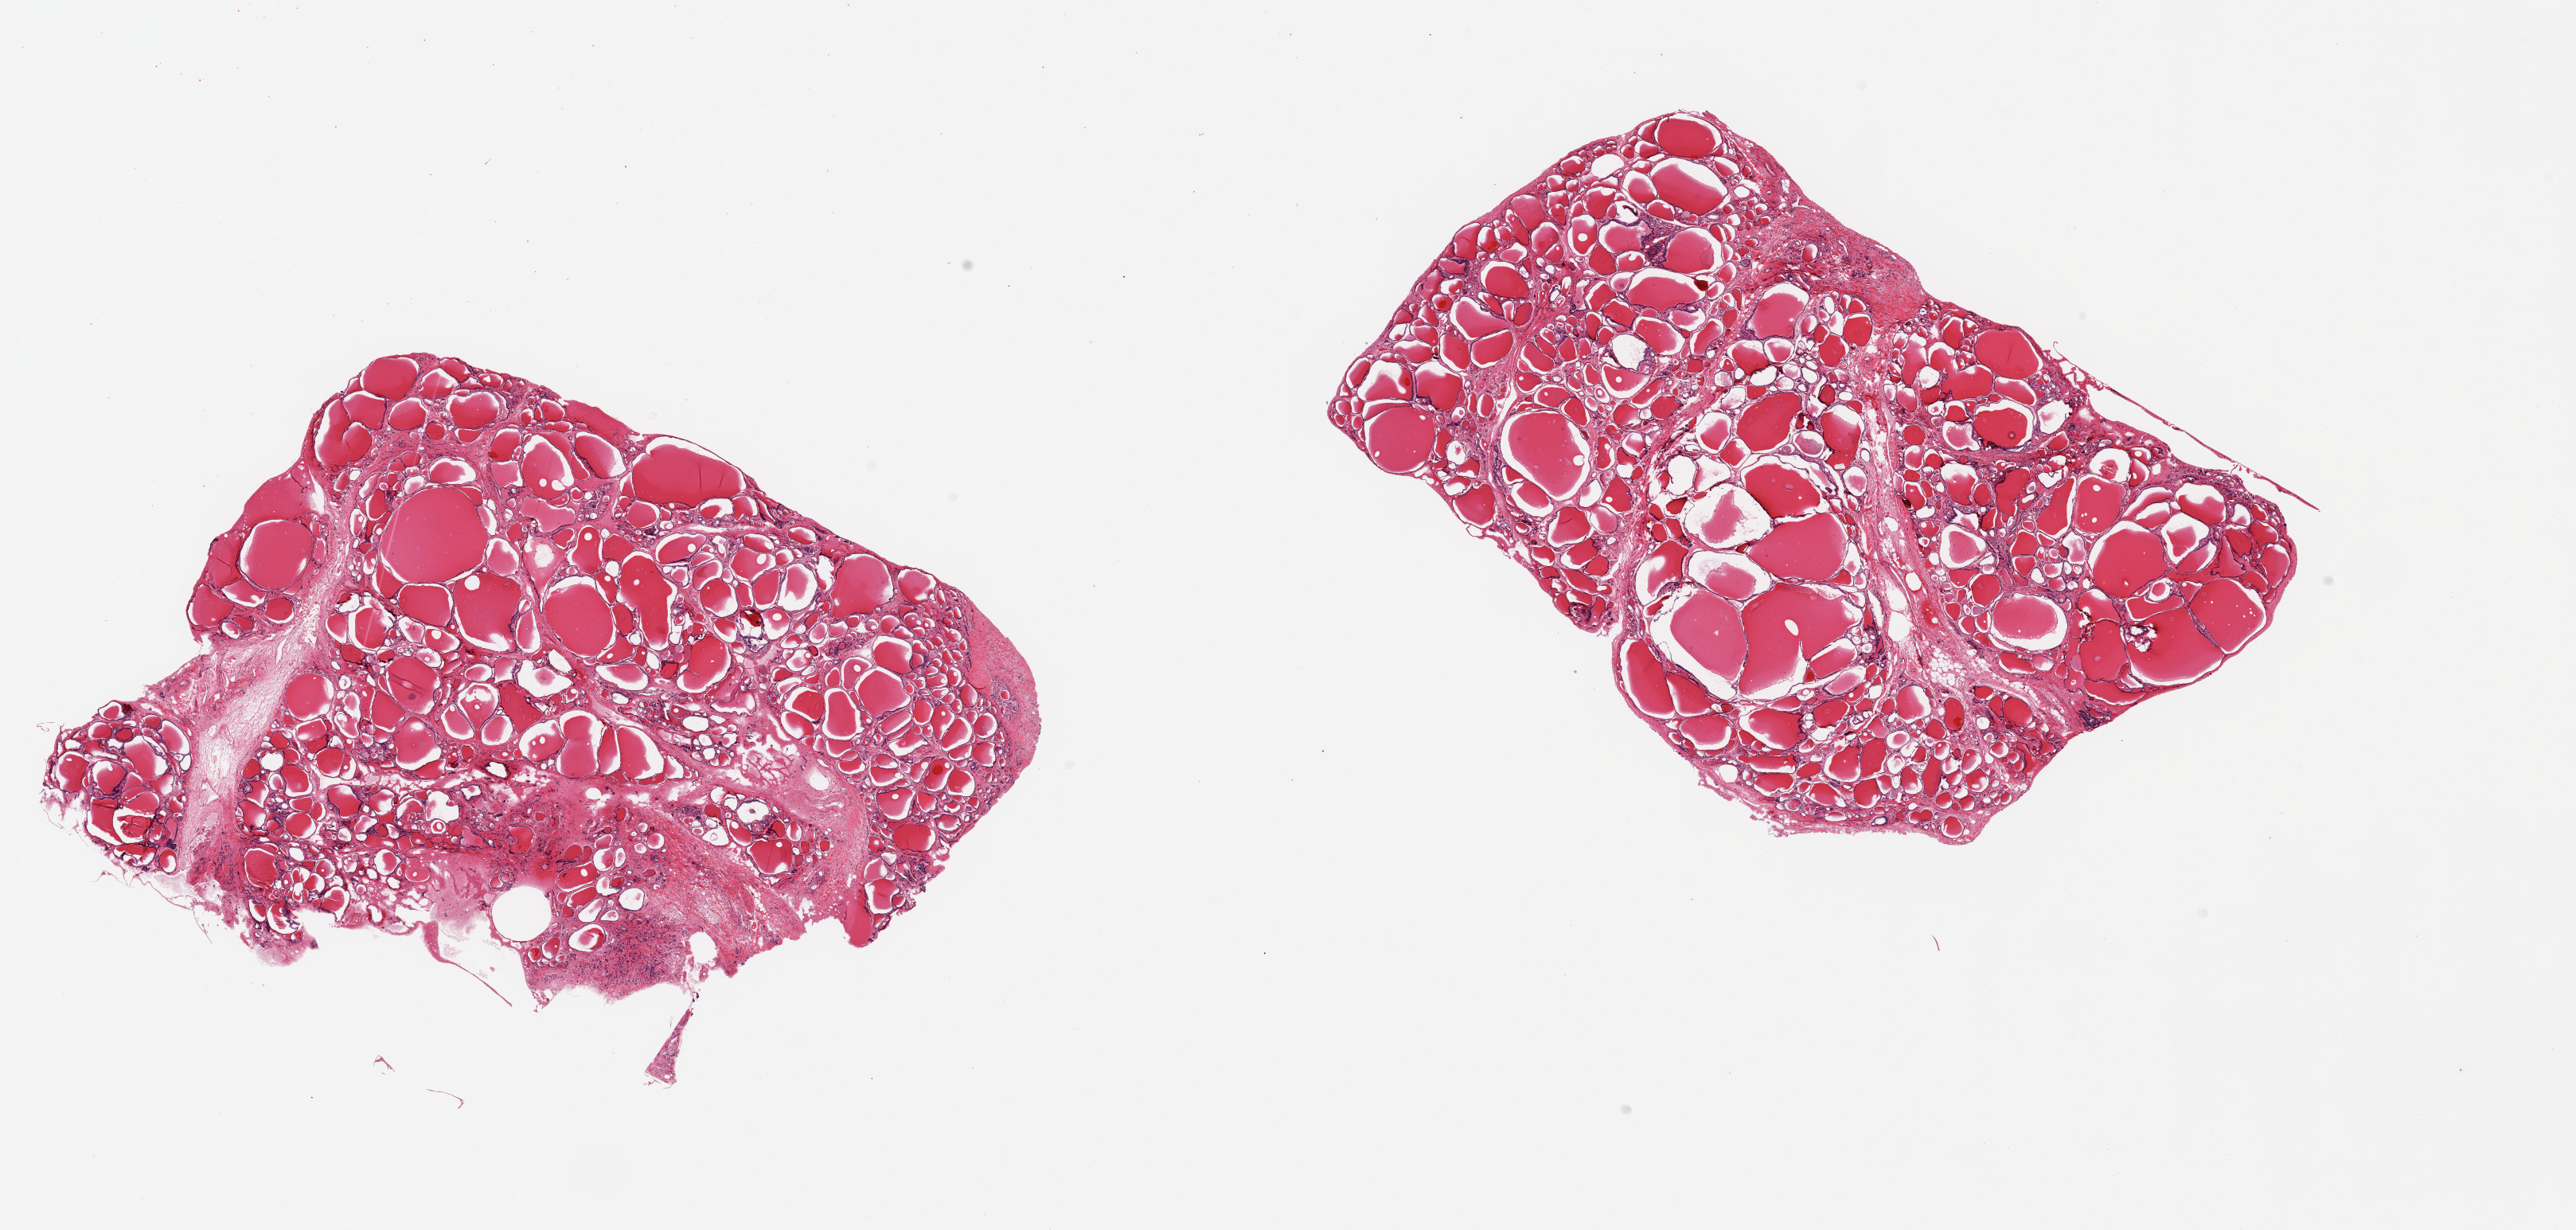
H&E whole-slide image, brightfield, whole scanned area (about 25.6 x 12.2 mm, from a 20x scan) shown as a low-resolution overview, PAXgene-fixed paraffin-embedded (PFPE) section, section of thyroid (target tissue), donor tissue sample. Donor sex: male.
• reviewer comment on this tissue sample: 2 pieces; foci of fibrosis up to 2.6 sq mm